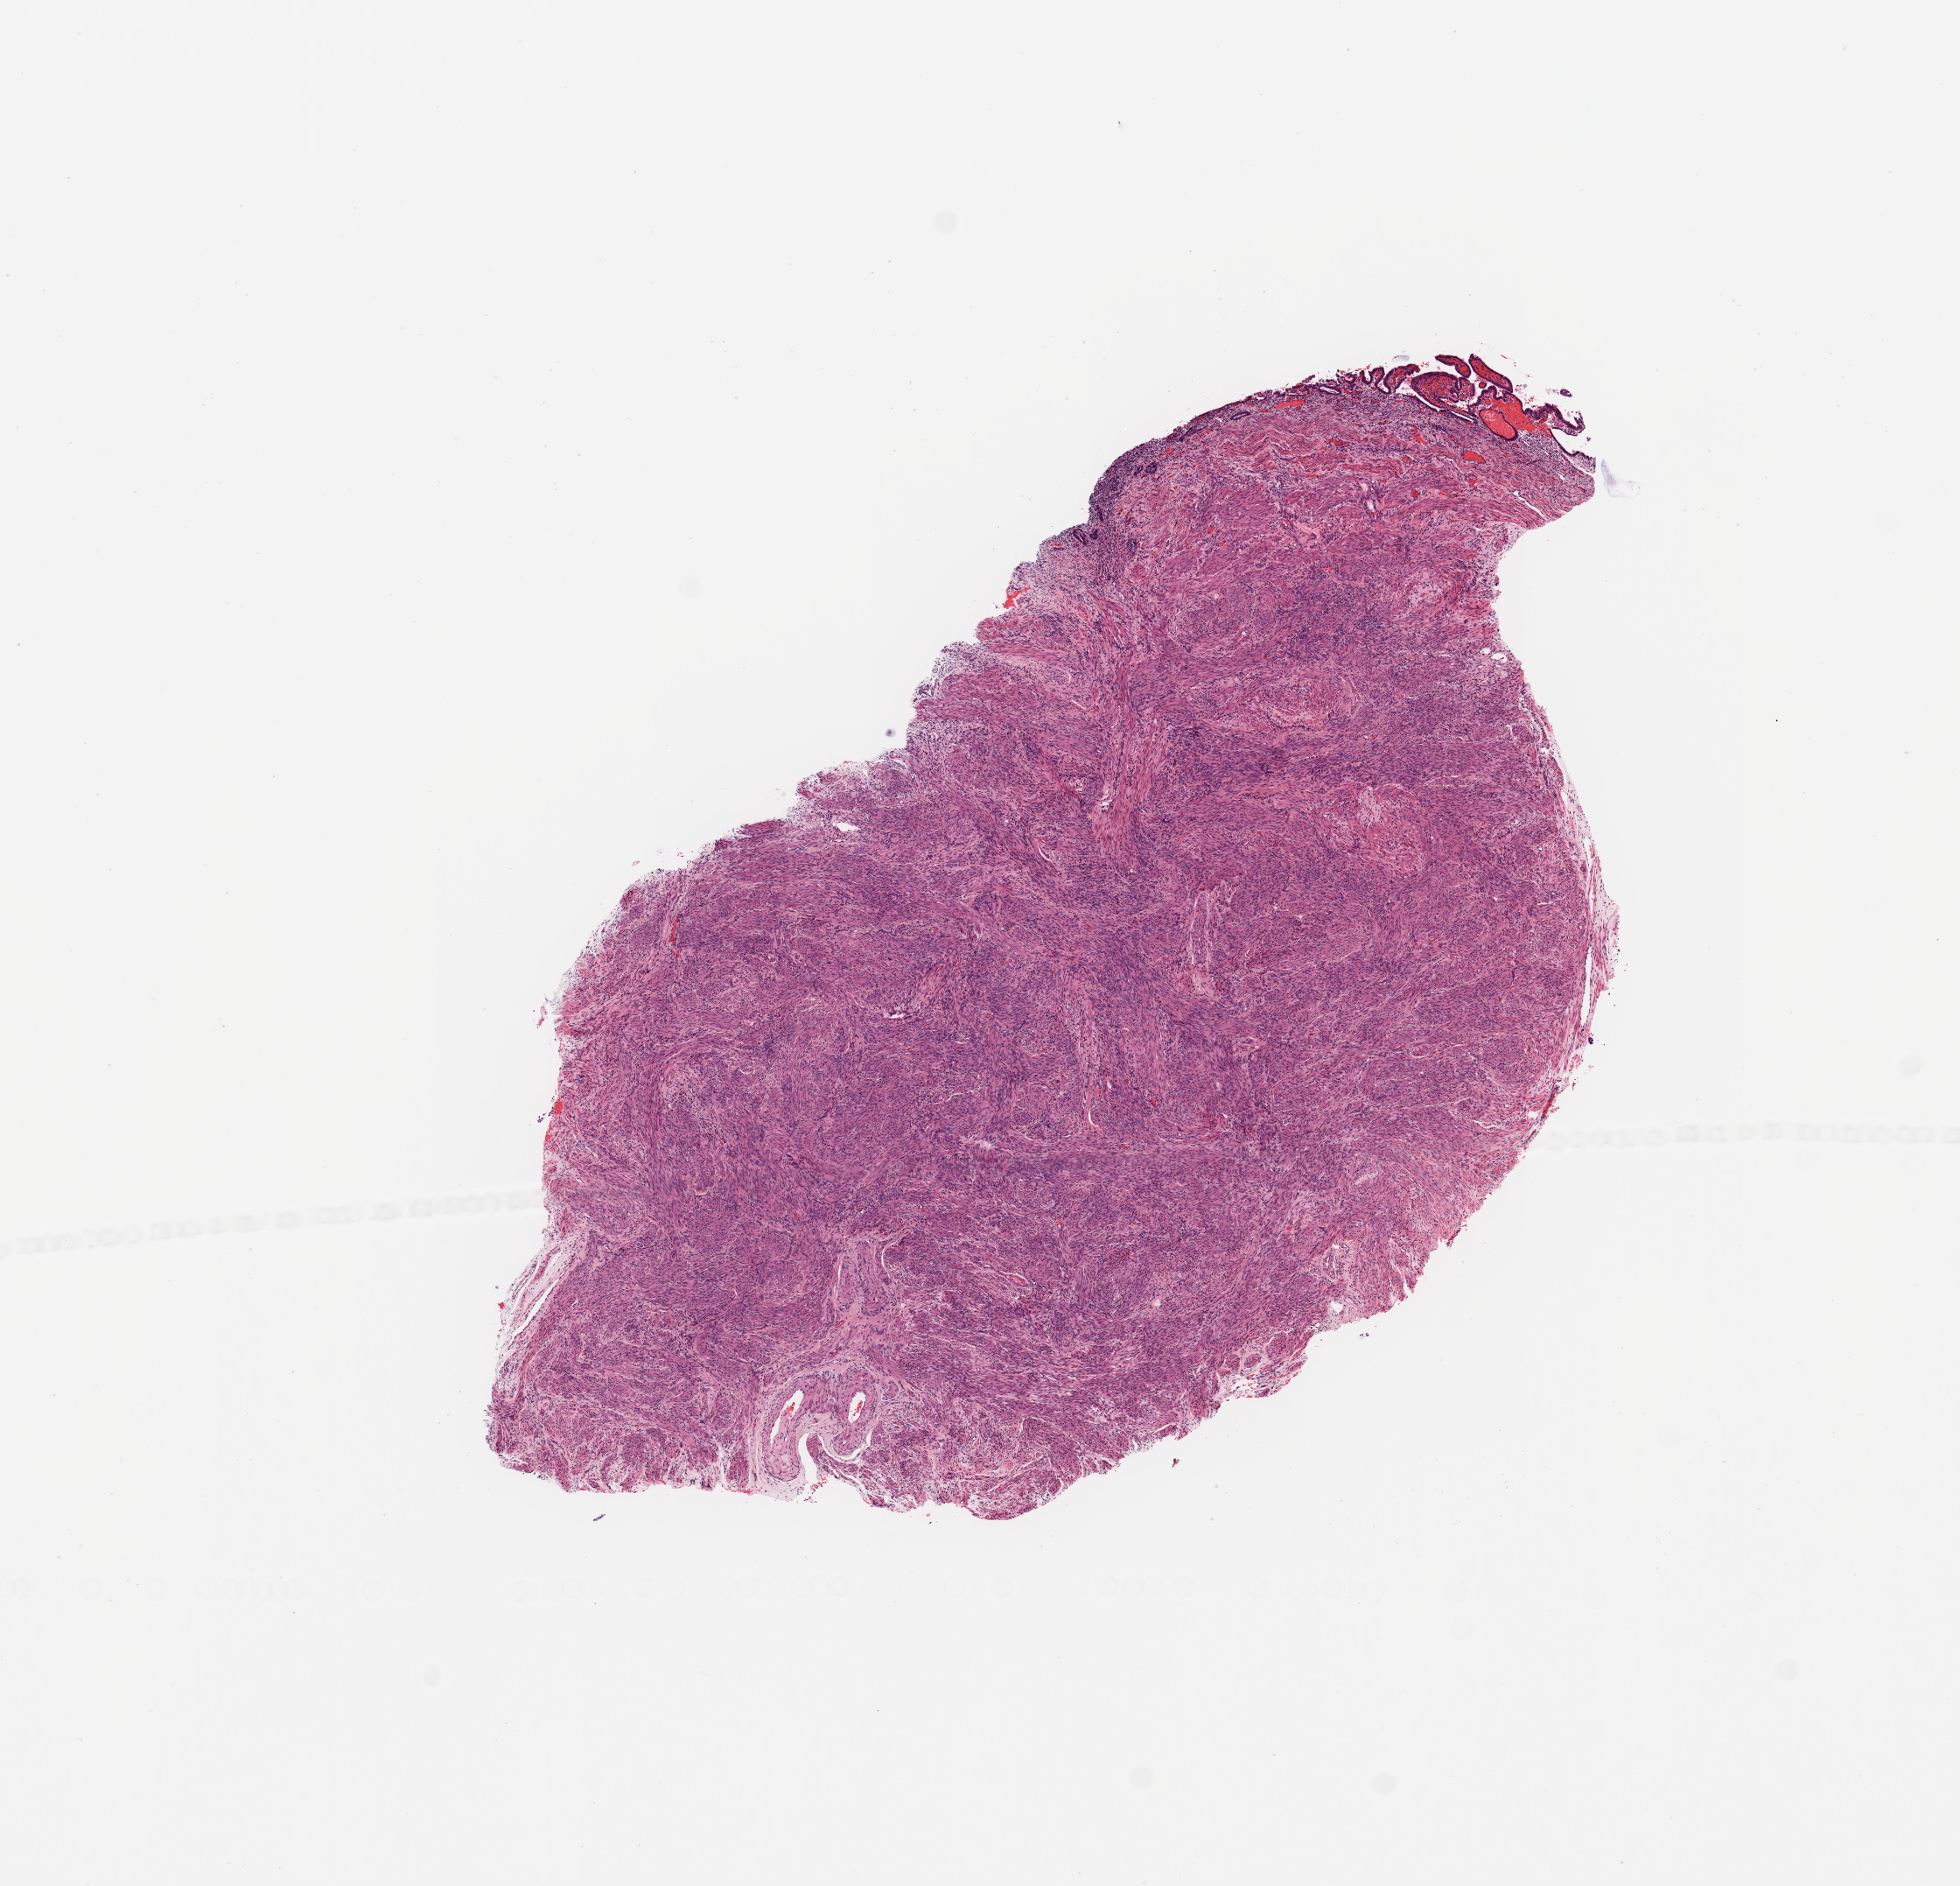
Whole-slide histology image, H&E-stained — shown as a low-resolution overview of the whole scanned area (about 8.9 x 8.5 mm, from a 20x scan). Normal (non-tumour) tissue sample, sampled site: uterus. 71-year-old female patient.
This section: normal (non-tumour) tissue from the same patient. Patient diagnosis: Endometrioid adenocarcinoma, NOS.